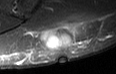
MRI of an extremity soft-tissue mass, one axial slice; position 13 of 36 along the scan axis; STIR; MR volume resampled by the dataset authors to the PET/CT grid (not the native acquisition matrix); 3.27 mm slice thickness; 116 × 74 image matrix, field of view 113 × 72 mm. Male patient. Case-level facts recorded for this patient, not image findings: histological type: pleiomorphic leiomyosarcoma; grade: high; site of the primary tumour: left buttock.
Structures marked on this image (expert contour drawn on MRI and transferred to this co-registered scan by the dataset authors):
- gross tumour volume including surrounding oedema: bounding box <34,22,81,52> (left, top, right, bottom; pixels)
- gross tumour volume (mass): <39,24,79,50>